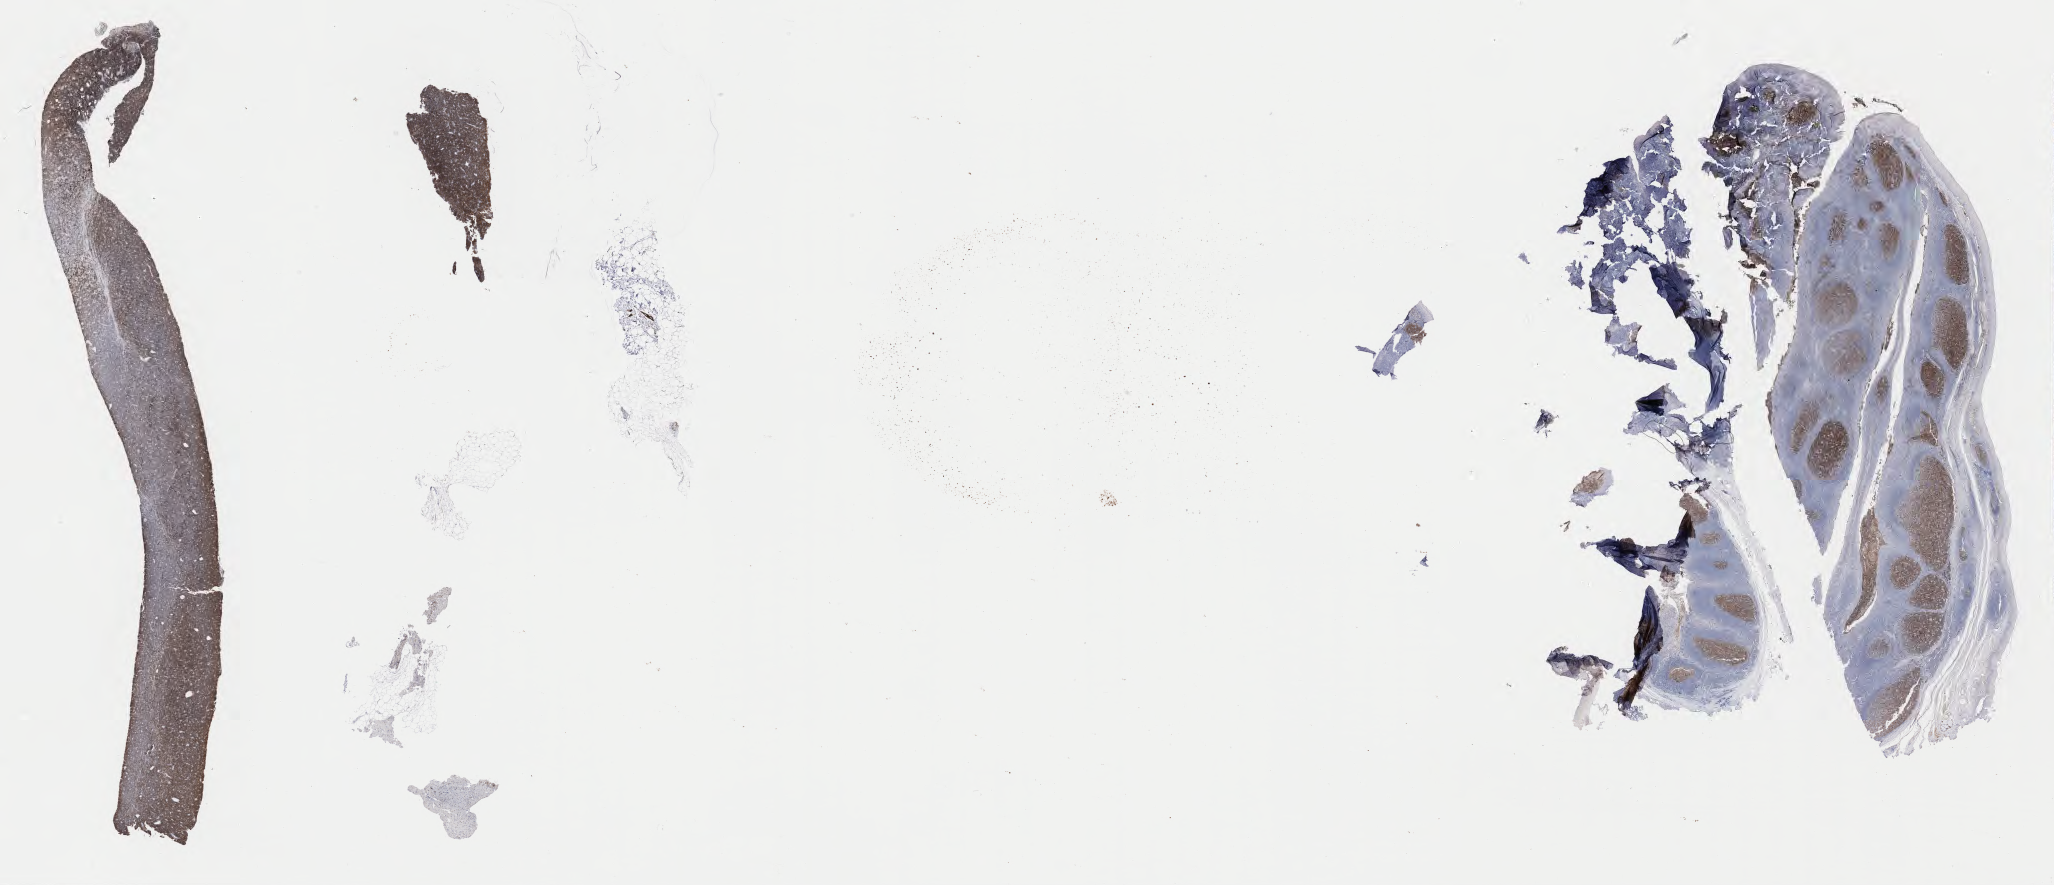
IHC for CD10, whole-slide image, low-resolution overview of the scanned area, about 33.2 x 14.3 mm, specimen: tumor tissue. Patient female; age 61 years.
Diagnosis: Burkitt lymphoma, NOS.